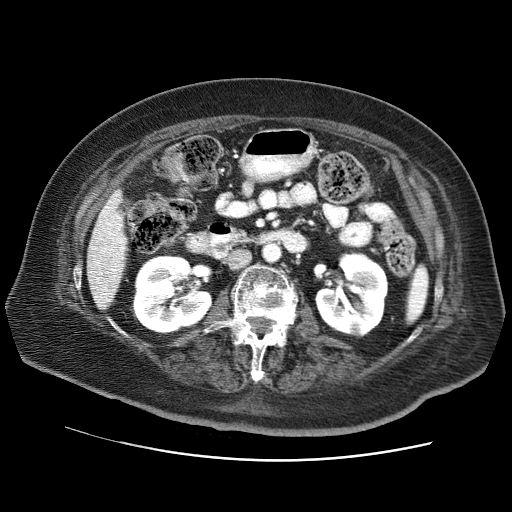
Contrast-enhanced abdominal CT (liver protocol), one axial slice. Slice 21 of 73 in the series (ordered by position). 120 kVp. Soft-tissue window (W 400 / L 40 HU). 2.5 mm slice thickness. 512 × 512 image matrix. Case-level facts recorded for this patient, not image findings: diagnosis: hepatocellular carcinoma (patient treated with transarterial chemoembolisation; whether this scan precedes or follows treatment is not stated here); TNM stage (as recorded): Stage-I; Child-Pugh class: A; tumour differentiation: well differentiated.
Structures marked on this image (semi-automatic segmentation, software-assisted and operator-edited):
- liver parenchyma outside the tumour (the mass and vessels are separate outlines, so this box may not span the whole liver): bounding box <86,190,126,308> (left, top, right, bottom; pixels)
- liver vessels: <96,206,123,302>